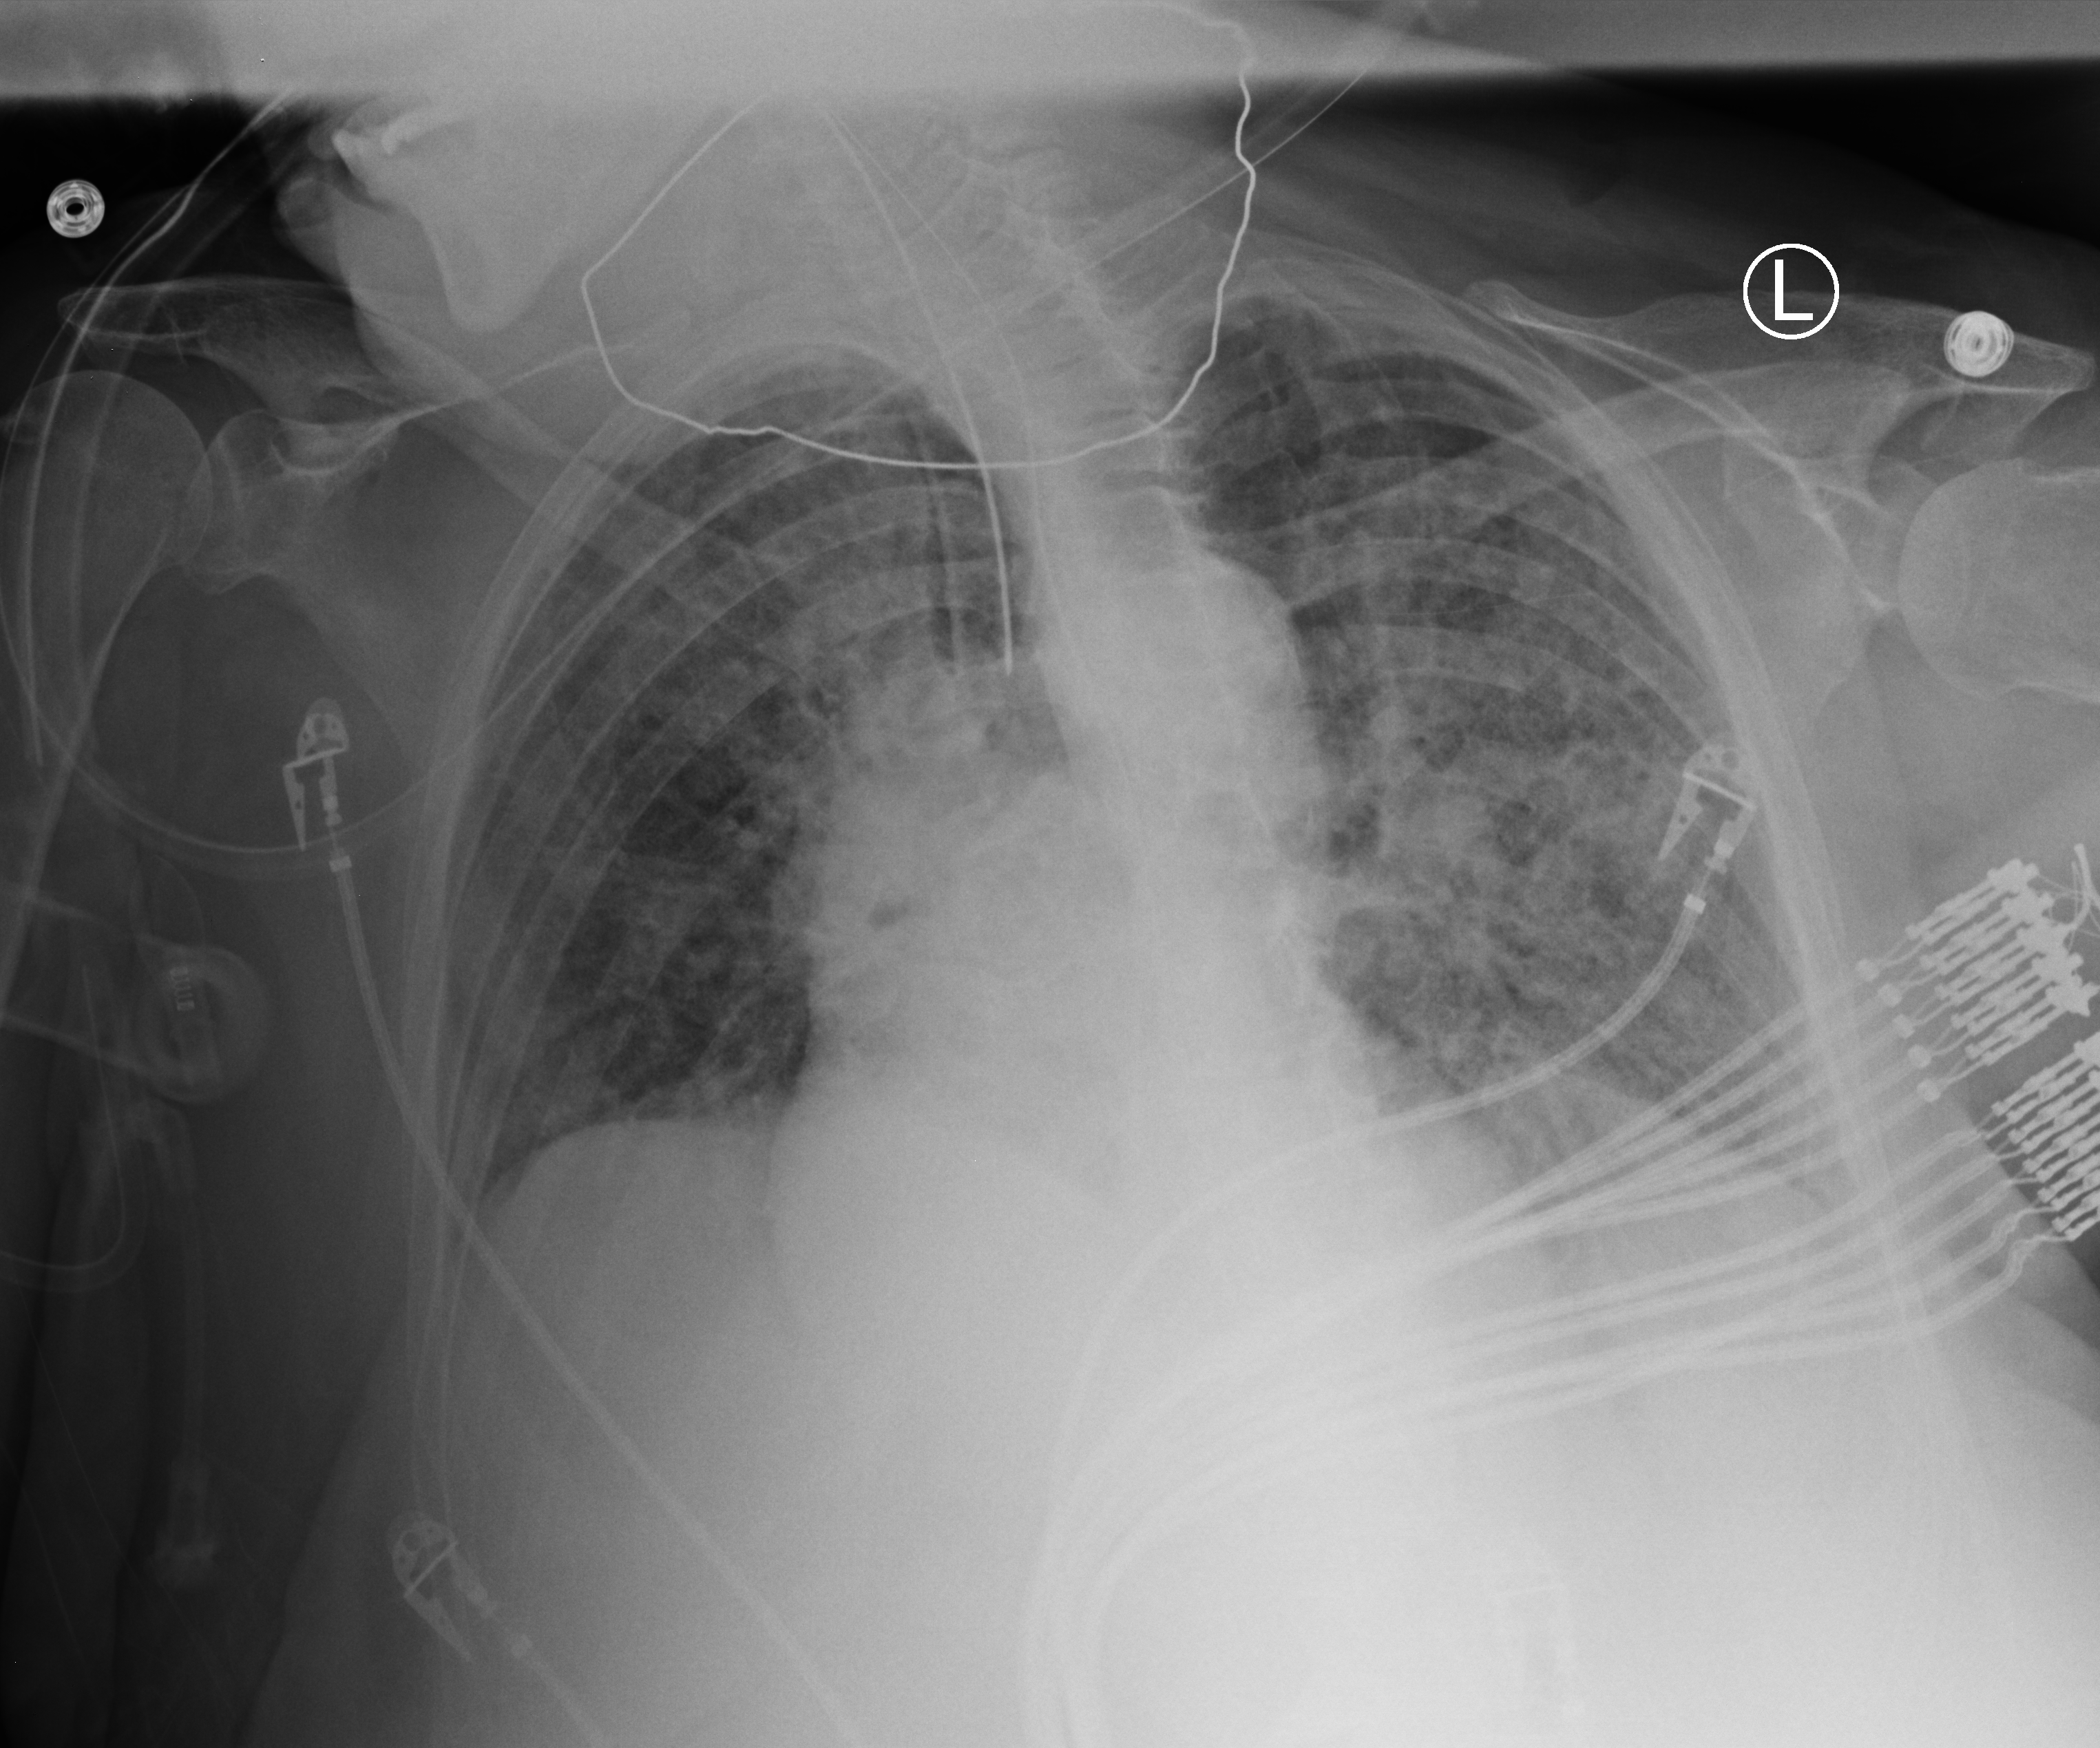
Chest X-ray (portable), anteroposterior (AP) projection. Patient hospitalised with COVID-19; female, aged 75–90 years.
Admission-level facts for this patient (not findings on this image; timing relative to this image not recorded):
- length of hospital stay: 28 days
- admitted to intensive care during this hospital stay: yes
- mechanically ventilated during this hospital stay: yes